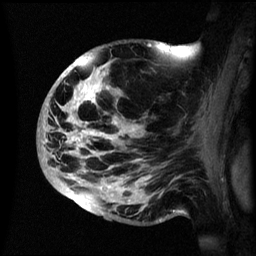
Breast MRI (dynamic contrast-enhanced), one sagittal slice; slice 36 of 60 in the series (ordered by position); dynamic contrast-enhanced series, image 2 of 3 at this slice position (ordered by acquisition); 1.5 T; TE 4.2 ms, TR 8.4 ms; 2.4 mm slice thickness; 256 × 256 image matrix. Female patient, age 48 years.
Outlined on this slice (semi-automatic segmentation, software-assisted and operator-edited):
- analysis volume of interest (the breast-tissue region the enhancement analysis was run in; not a lesion): bounding box <38,42,195,222> (left, top, right, bottom; pixels)
- tumour enhancement mask (voxels above the 70 % enhancement threshold inside the analysis volume of interest): <43,56,134,212>